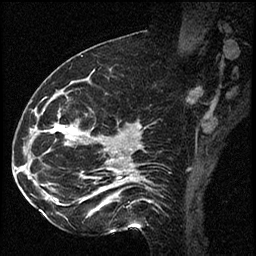
Breast MRI (dynamic contrast-enhanced), one sagittal slice. Dynamic contrast-enhanced series, image 2 of 2 at this slice position (ordered by acquisition). 1.5 T. TE 4.2 ms, TR 17.3 ms. 256 × 256 image matrix, field of view 200 × 200 mm. Female patient. Case-level facts recorded for this patient, not image findings: setting: breast cancer imaged before/during neoadjuvant chemotherapy; receptor status: HR-positive, HER2-negative.
Outlined on this slice (semi-automatically segmented with operator editing):
- analysis volume of interest (the breast-tissue region the enhancement analysis was run in; not a lesion): bounding box <41,93,115,223> (left, top, right, bottom; pixels)
- tumour enhancement mask (voxels above the 100 % enhancement threshold inside the analysis volume of interest): <56,127,74,131>